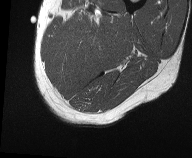
MRI of an extremity soft-tissue mass, one axial slice. Position 8 of 61 along the scan axis. MR volume resampled by the dataset authors to the PET/CT grid (not the native acquisition matrix). 192 × 158 image matrix, field of view 187 × 154 mm. Male patient. From the clinical record (not read from this slice): histological type: pleiomorphic liposarcoma; grade: high; site of the primary tumour: left thigh.
Annotated regions visible in this slice (expert contour drawn on MRI and transferred to this co-registered scan by the dataset authors):
- gross tumour volume including surrounding oedema: box from (x=73, y=12) to (x=112, y=45) px